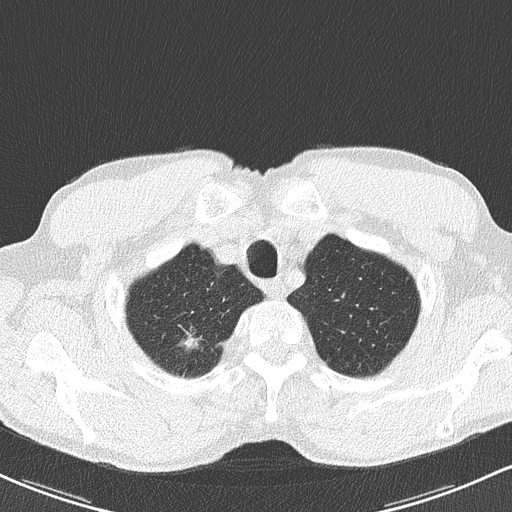
Low-dose screening chest CT, axial slice. Baseline screening round. Lung window (W 1500 / L -600 HU). Lung (sharp) reconstruction kernel (B50f). 120 kVp. Male participant, aged 62 years at enrolment. Former smoker at enrolment.
- Expert-annotated lung lesion, bounding box <166,326,212,368> (left, top, right, bottom; pixels).
- Screening reader's record for this exam (one nodule recorded; not confirmed to be the boxed lesion): non-calcified nodule or mass ≥4 mm, right upper lobe, 12 × 9 mm, spiculated (stellate) margins, soft tissue attenuation.
- Lung cancer was diagnosed 398 days after this screen (after the second annual screen): bronchiolo-alveolar adenocarcinoma, NOS, right upper lobe, well differentiated (G1), stage IA (AJCC 6th edition), 15 mm at pathology.